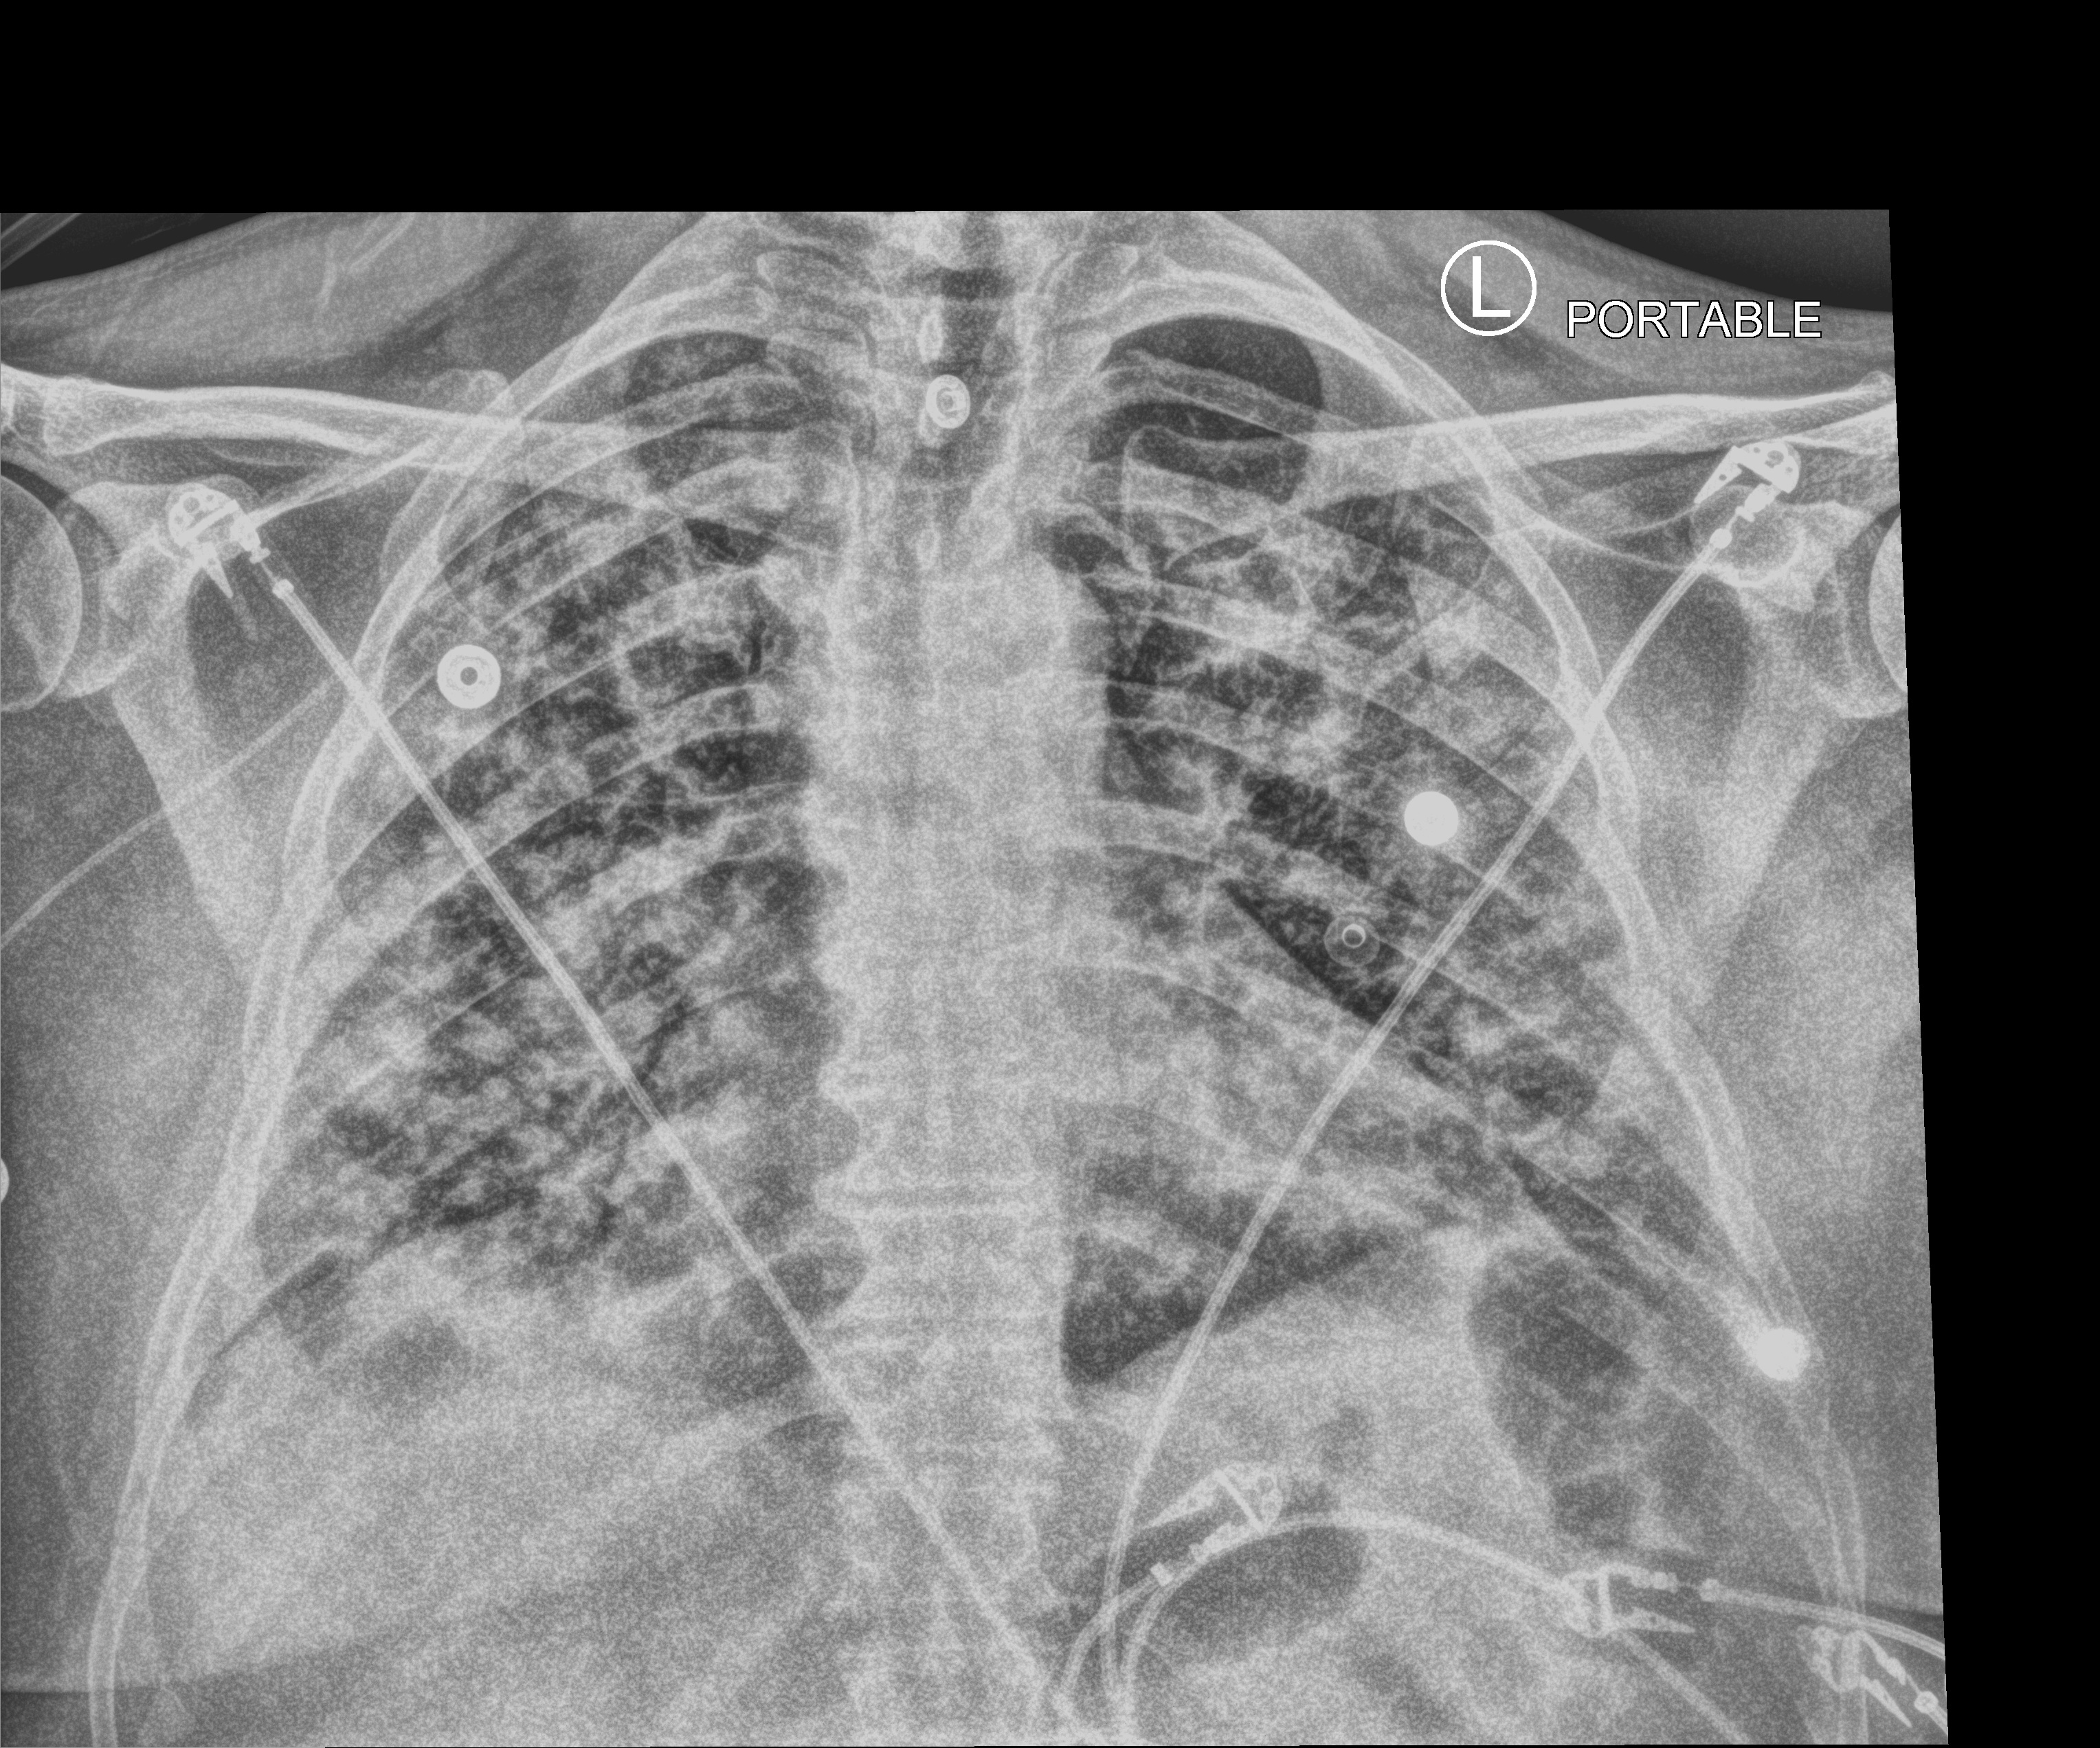
Portable chest radiograph, anteroposterior (AP) projection. Patient hospitalised with COVID-19; male, aged 18–59 years.
Admission-level facts for this patient (not findings on this image; timing relative to this image not recorded):
- mechanically ventilated during this hospital stay: no
- length of hospital stay: 12 days